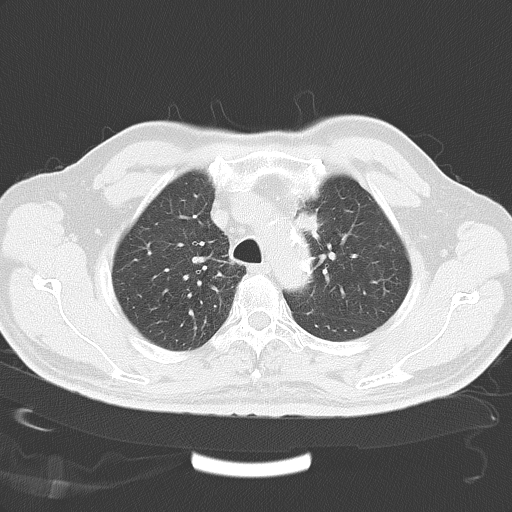
Chest CT, one axial slice; position 41 of 51 along the scan axis; reconstruction kernel B70f; lung window (W 1500 / L -600 HU); 5 mm slice thickness; 512 × 512 image matrix, field of view 357 × 357 mm. Patient: male, 67 years. From the clinical record (not read from this slice): clinical TNM (as recorded): T1a N2 M1a.
Annotated regions visible in this slice (rectangle marked by the reading radiologist):
- lung tumour (recorded histology: large cell carcinoma): bounding box <292,207,324,236> (left, top, right, bottom; pixels)